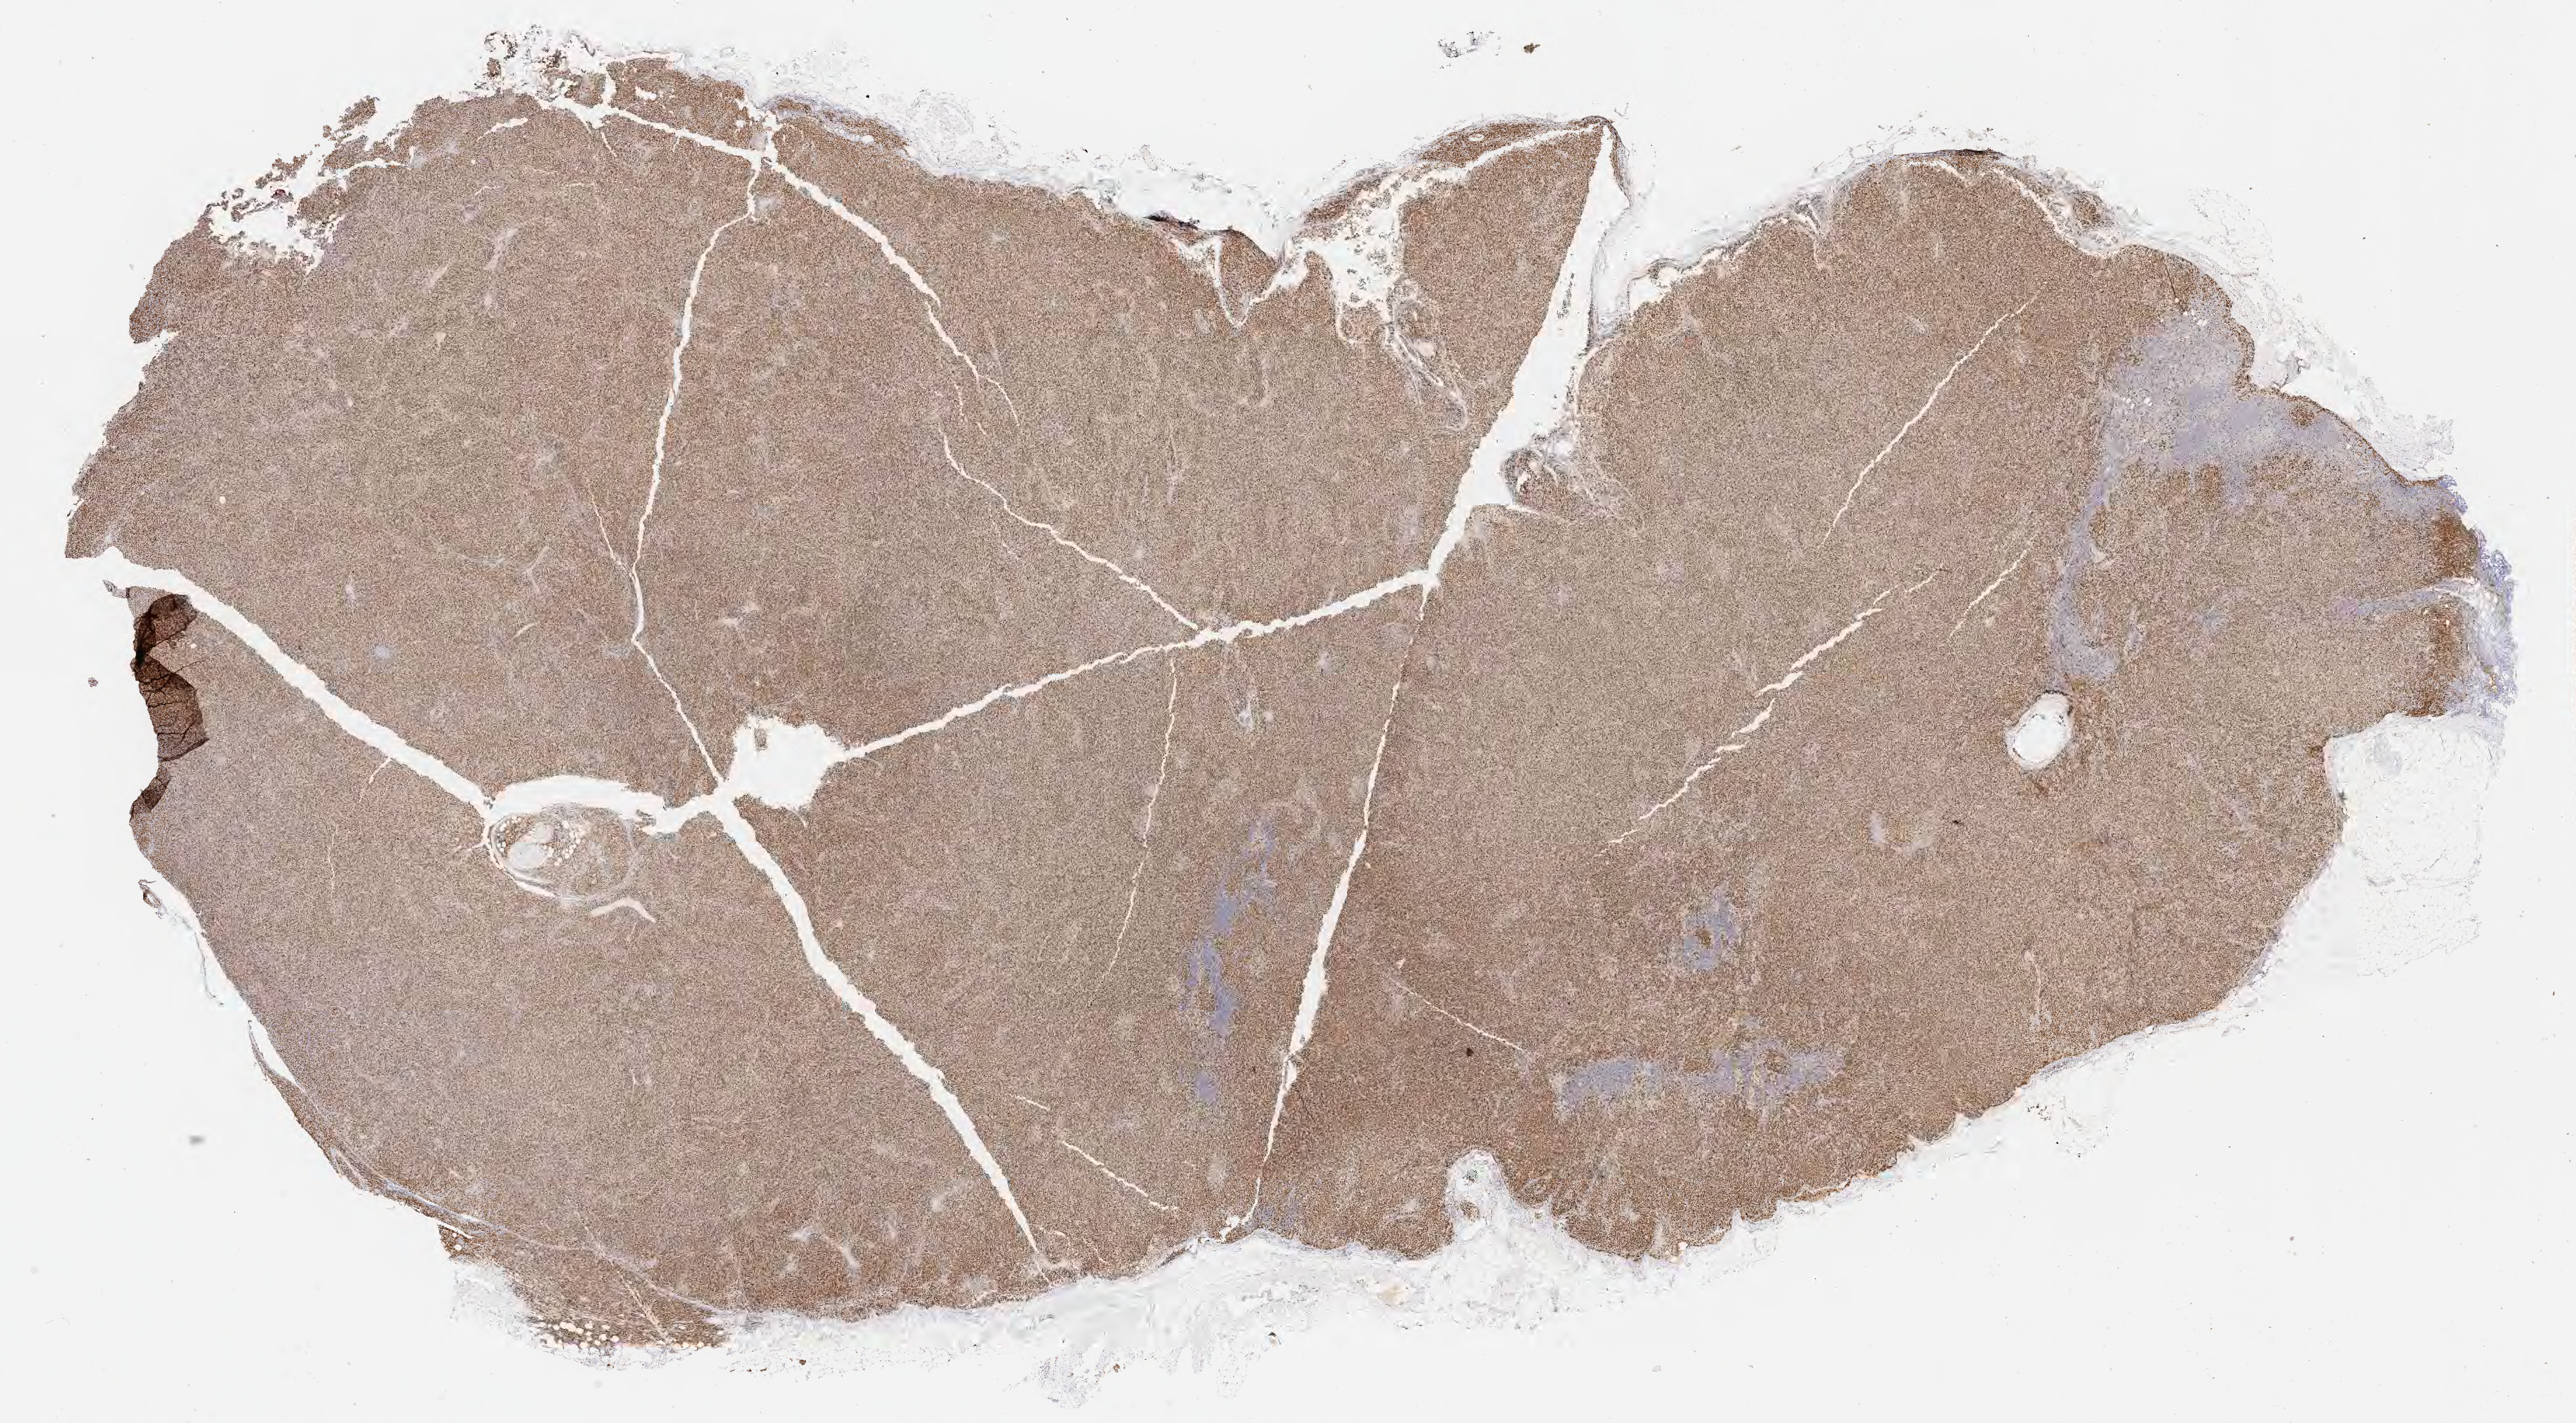
Whole-slide image, immunohistochemical stain for Ki-67 — a low-resolution overview of the entire scanned area, about 29.7 x 16.4 mm, specimen: tumor tissue. Patient male; age 69 years.
Histologic diagnosis: Diffuse large B-cell lymphoma, NOS.